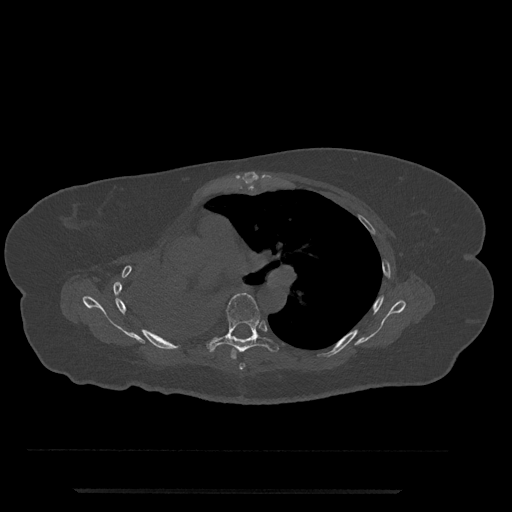
CT including the spine, one axial slice; reconstruction kernel Br40s/3; 120 kVp; bone window (W 1800 / L 400 HU); 0.5 mm slice thickness; 512 × 512 image matrix, field of view 440 × 440 mm. Female patient, age 51 years. Case-level facts recorded for this patient, not image findings: primary cancer: neuro; vertebrae with lytic lesions (as recorded): T8.
Outlined on this slice (semi-automatically segmented with operator editing):
- T5 vertebra: box from (x=239, y=363) to (x=245, y=370) px
- T6 vertebra: (x=207, y=293)–(x=279, y=359)